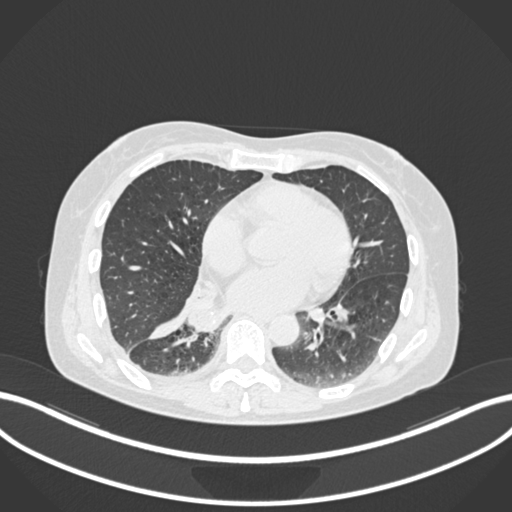
Chest CT, one axial slice. Position 66 of 168 along the scan axis. Reconstruction kernel B30f. 120 kVp. Lung window (W 1500 / L -600 HU). 1 mm slice thickness. 512 × 512 image matrix, field of view 400 × 400 mm. Patient: female, 63 years. Case-level facts recorded for this patient, not image findings: clinical TNM (as recorded): T1c N0 M0.
Structures marked on this image (rectangle marked by the reading radiologist):
- lung tumour (recorded histology: adenocarcinoma): bounding box <177,287,236,332> (left, top, right, bottom; pixels)